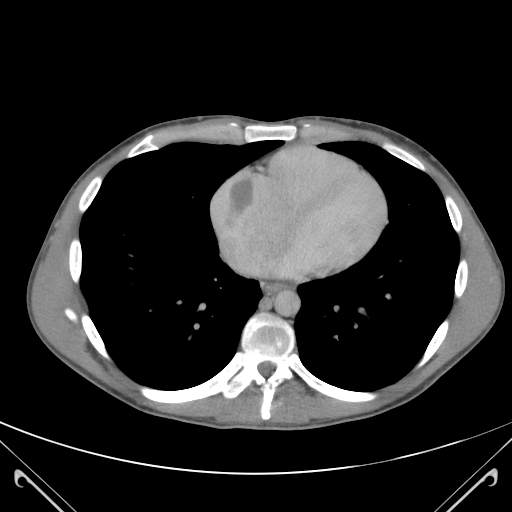
Contrast-enhanced abdominal CT (liver protocol), one axial slice. Position 117 of 118 along the scan axis. Soft-tissue window (W 400 / L 40 HU). 512 × 512 image matrix. From the clinical record (not read from this slice): diagnosis: hepatocellular carcinoma (patient treated with transarterial chemoembolisation; whether this scan precedes or follows treatment is not stated here); TNM stage (as recorded): Stage-IIIB; Child-Pugh class: A; tumour nodularity: uninodular.
Outlined on this slice (semi-automatically segmented with operator editing):
- abdominal aorta: box from (x=274, y=290) to (x=299, y=315) px